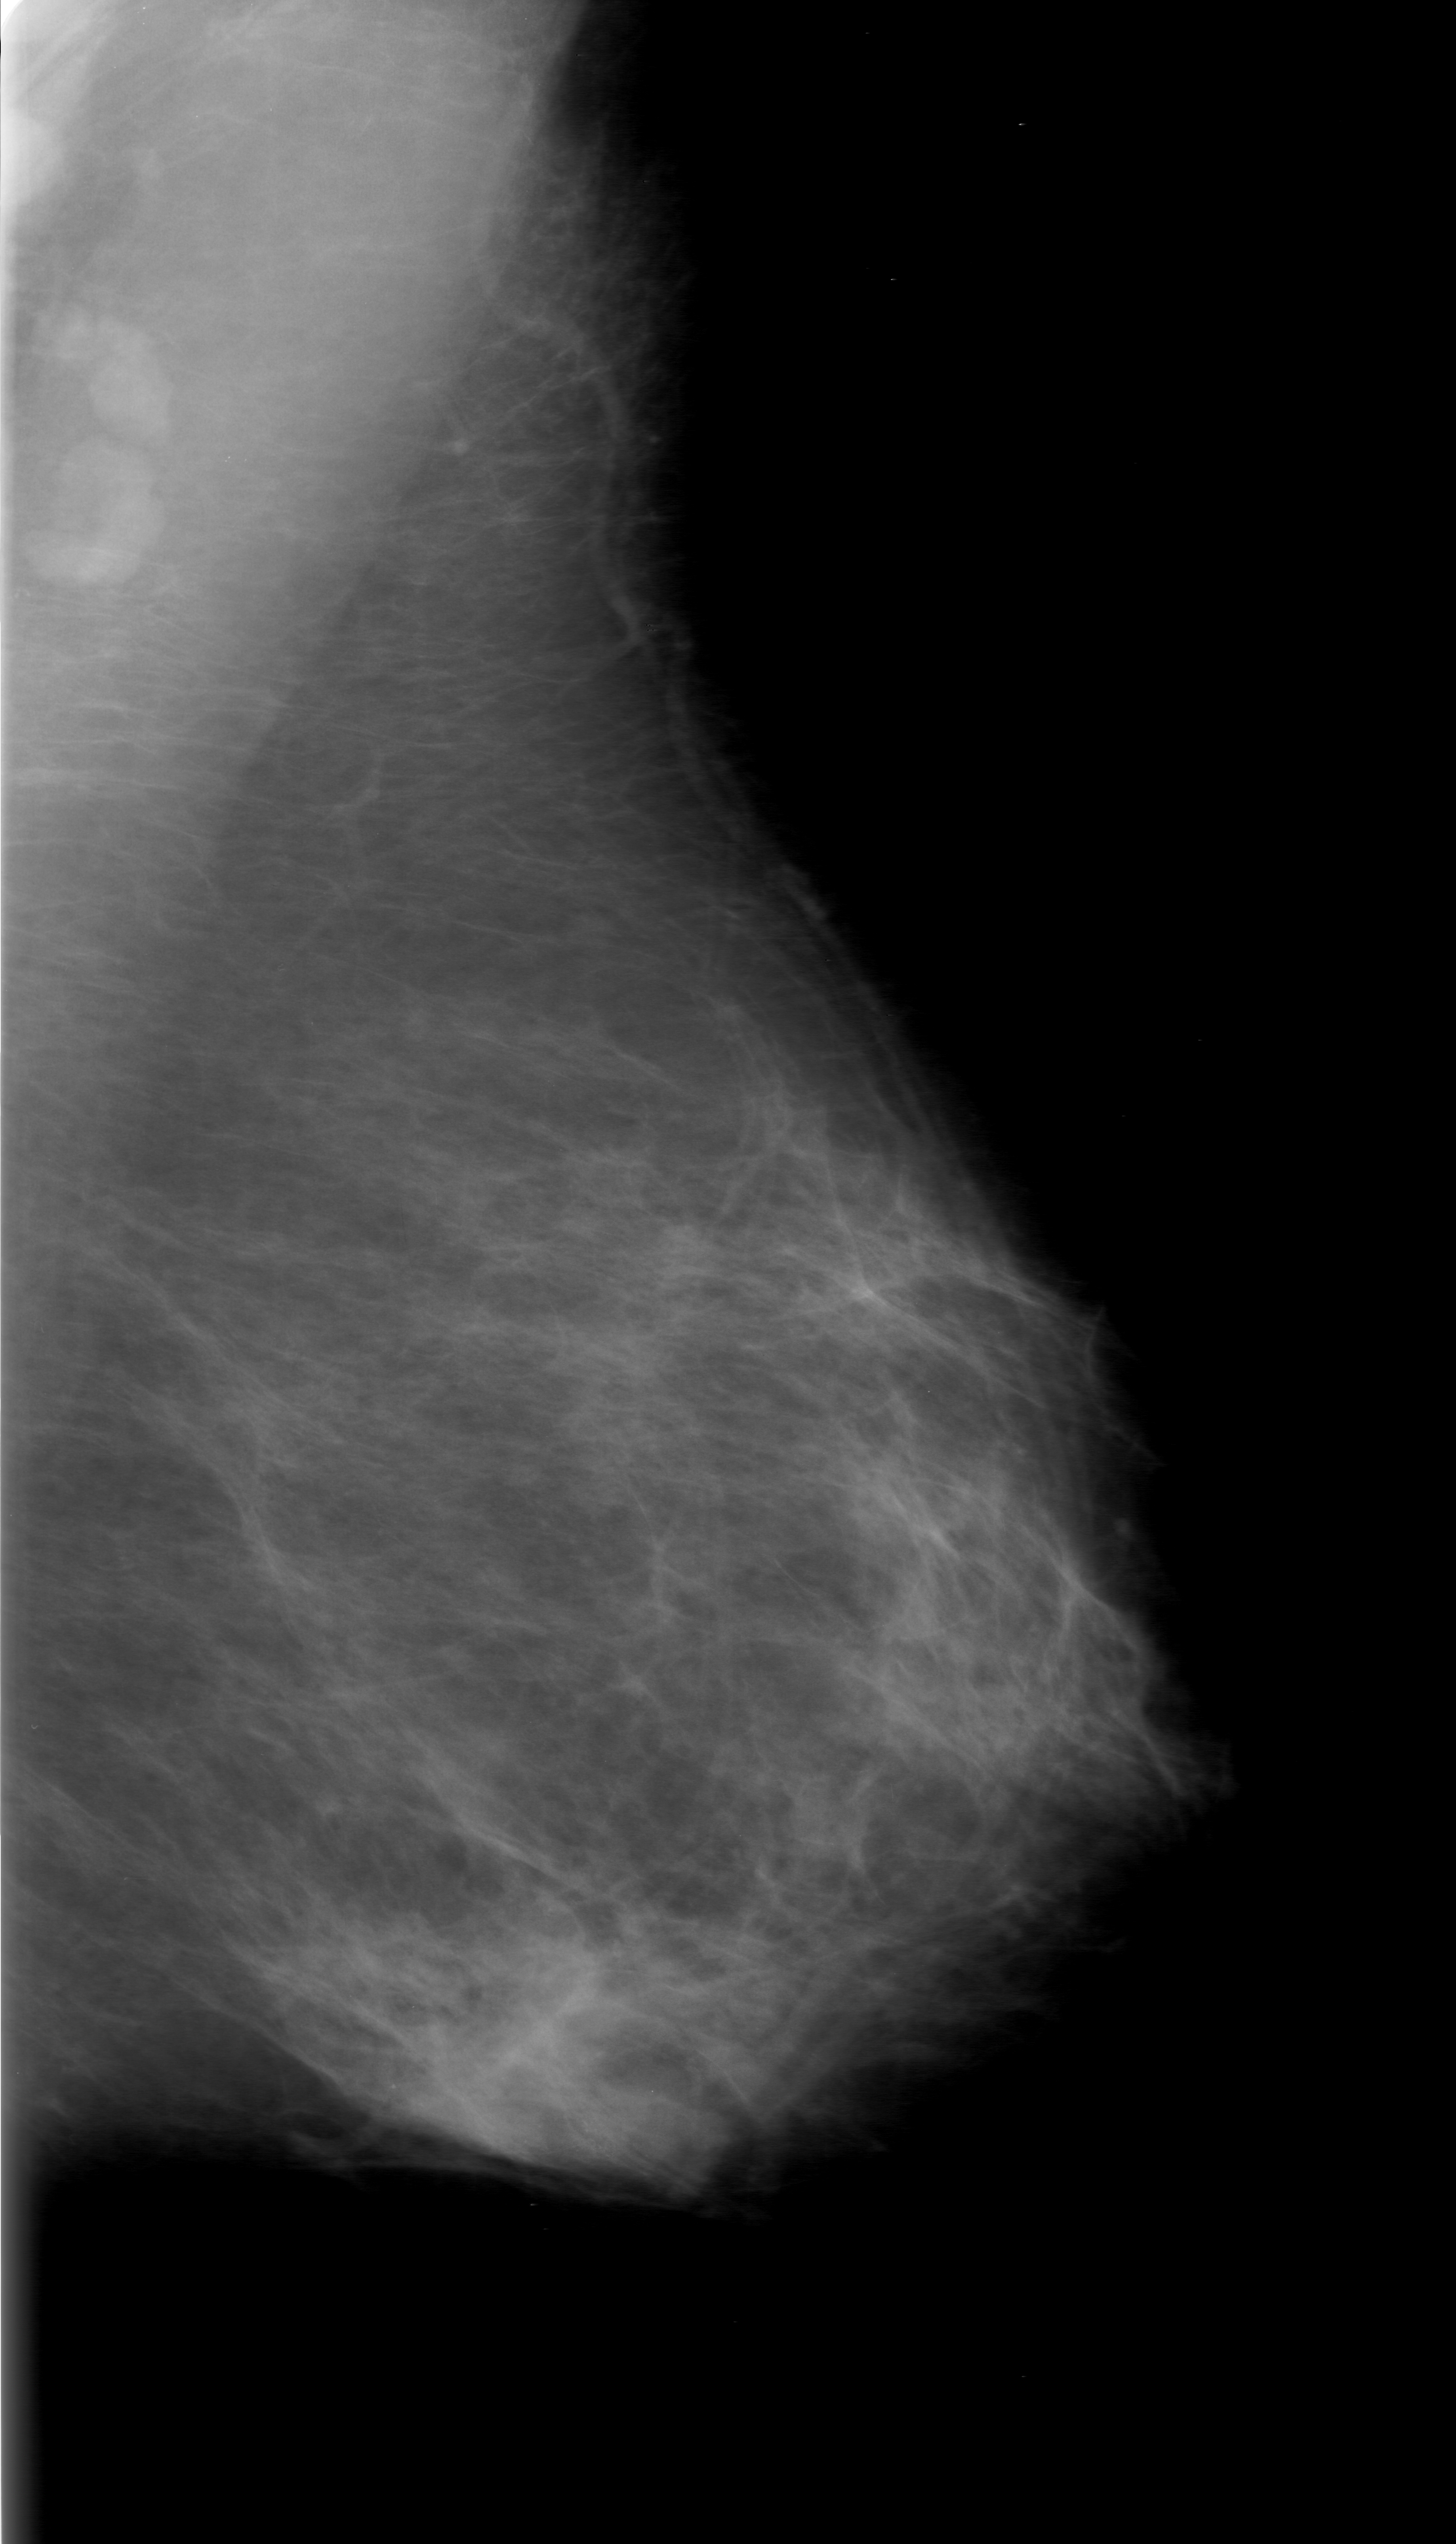
Scanned film-screen mammogram; left breast; mediolateral oblique (MLO) view; BI-RADS breast density category 2 (scale 1–4); 1456 × 2544 image matrix.
Expert-marked regions of interest on this image (one box per marked abnormality):
- calcifications, morphology amorphous, distribution clustered; BI-RADS assessment category 0 (incomplete: needs additional imaging); pathology (as recorded): malignant: bounding box (x1, y1, x2, y2) in pixels: (488, 2022, 716, 2213)